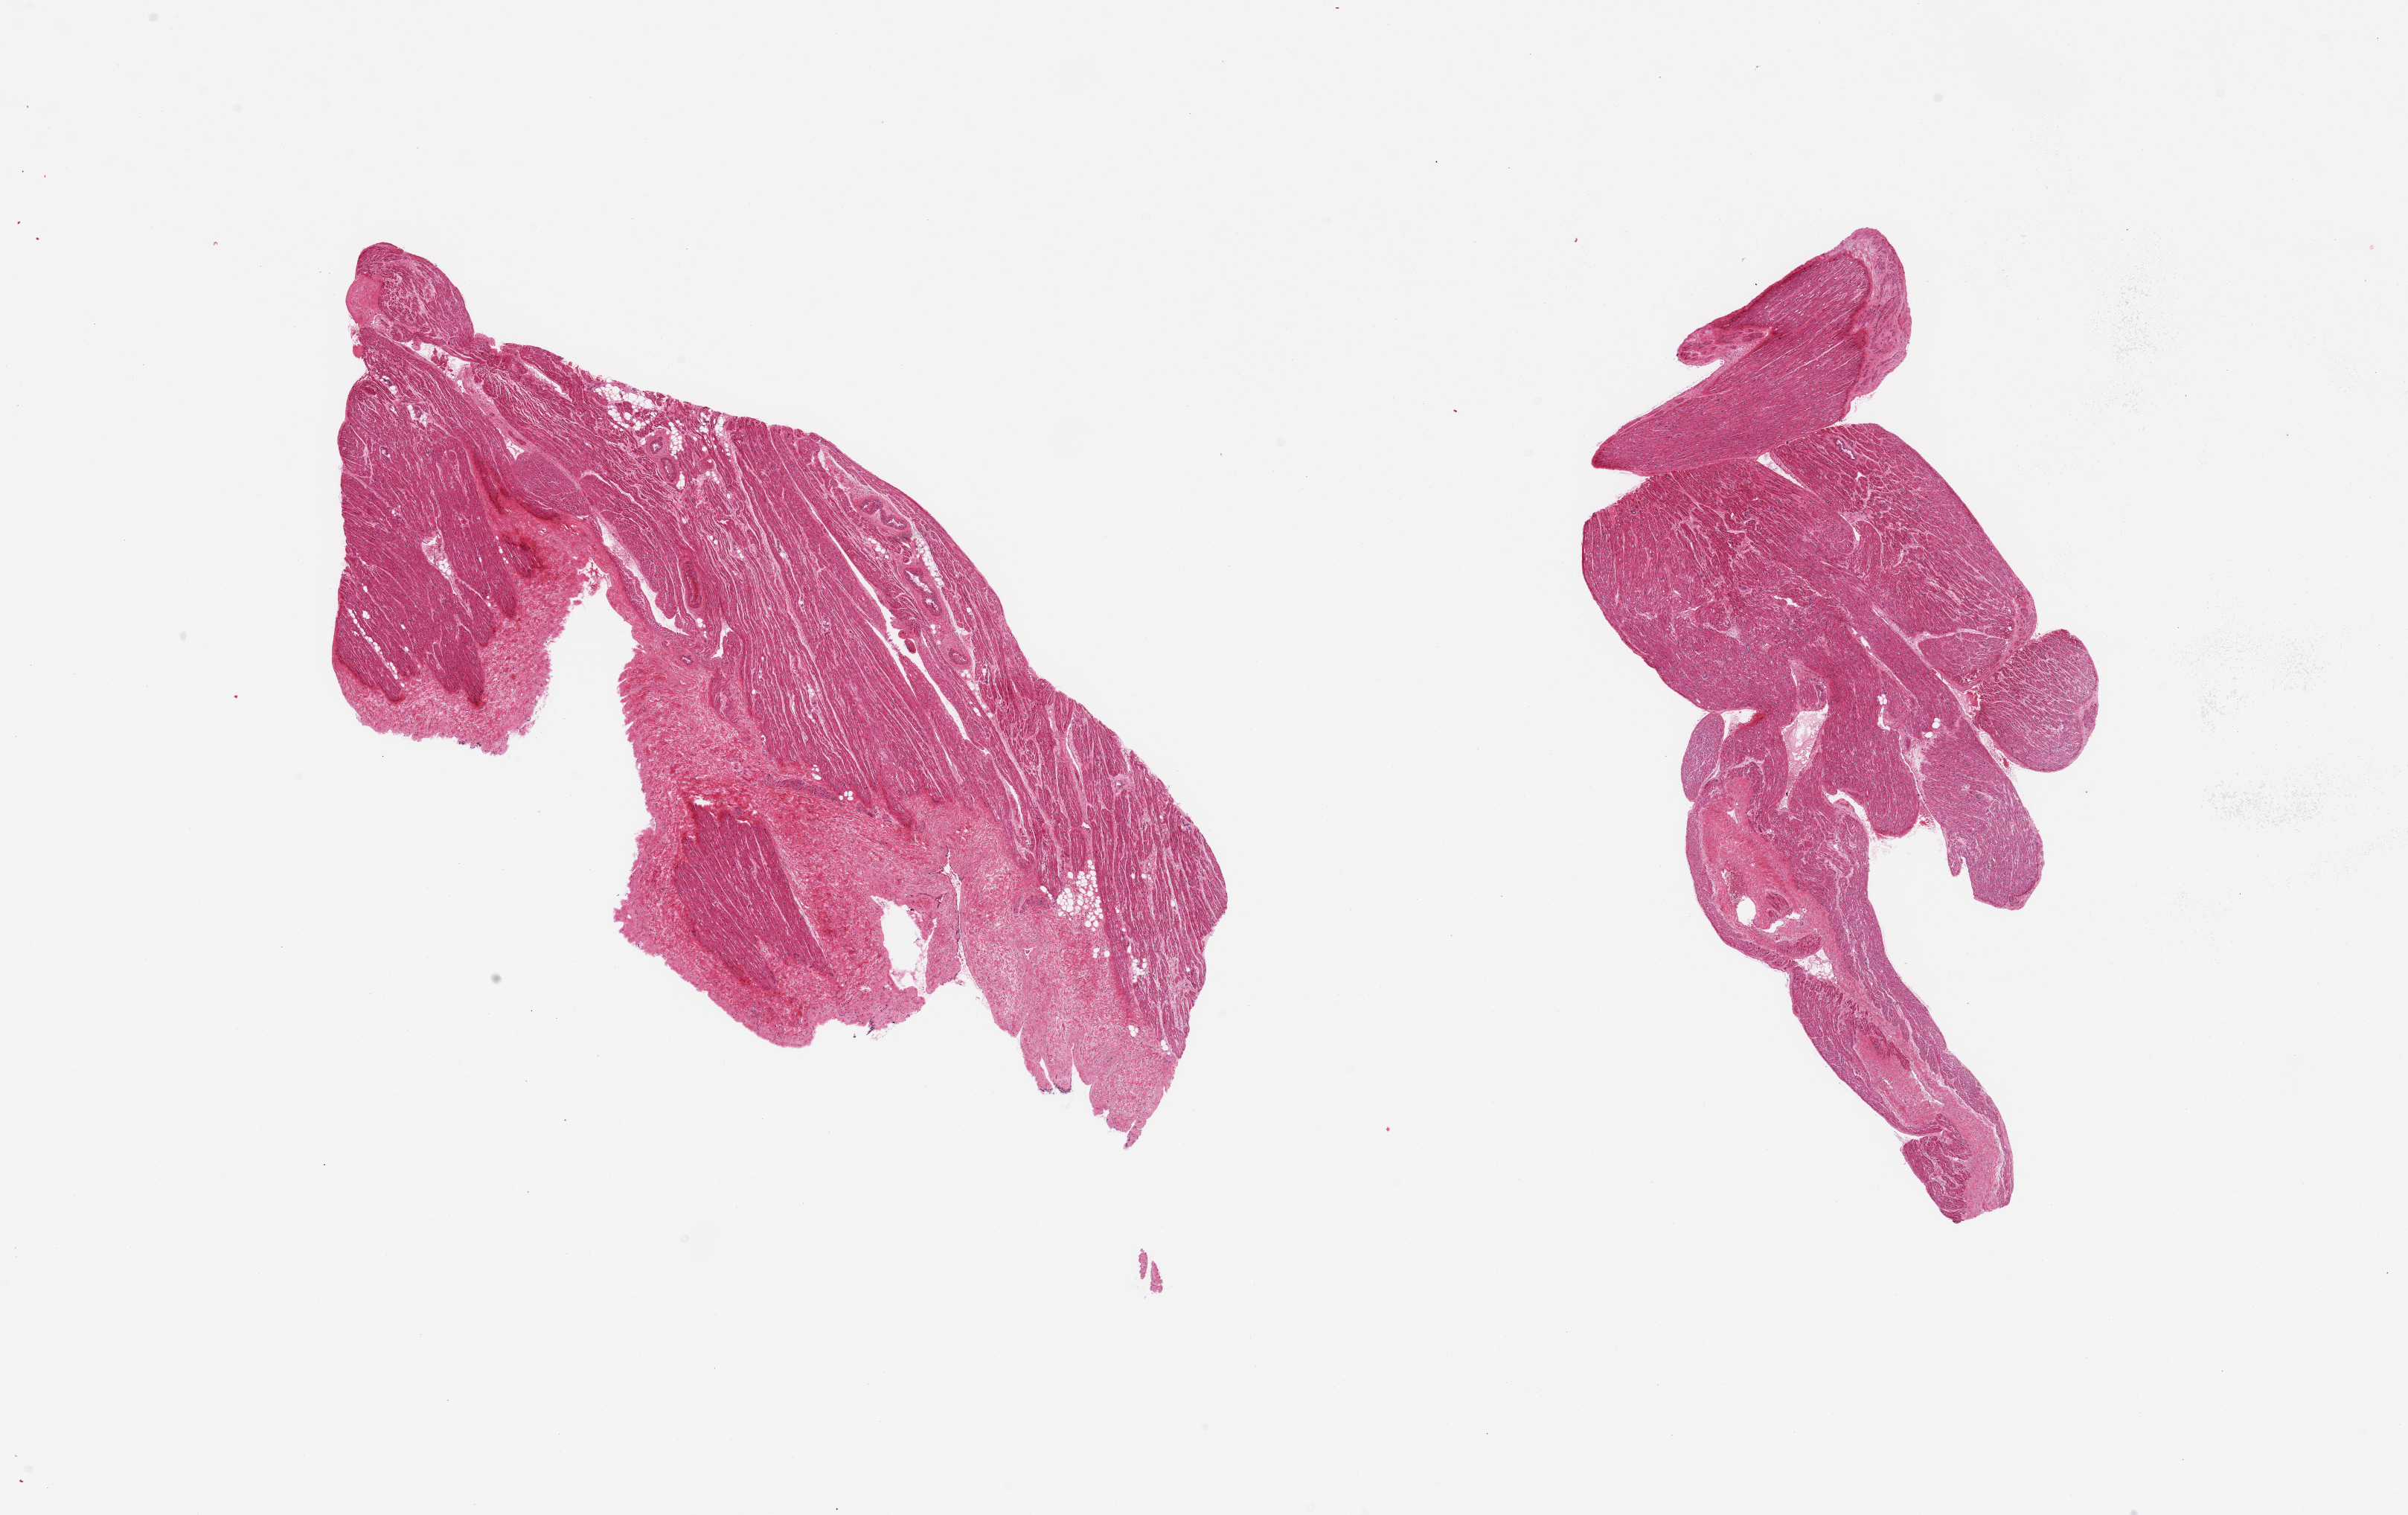
Whole-slide image, H&E stain — shown as a low-resolution overview of the whole scanned area (about 25.6 x 16.1 mm), PAXgene-fixed paraffin-embedded (PFPE) section, sampled site (target tissue): auricular appendage, tissue donor sample. Male donor.
Review note (as recorded): 2 pieces; essentially well trimmed fibromuscular tissue.